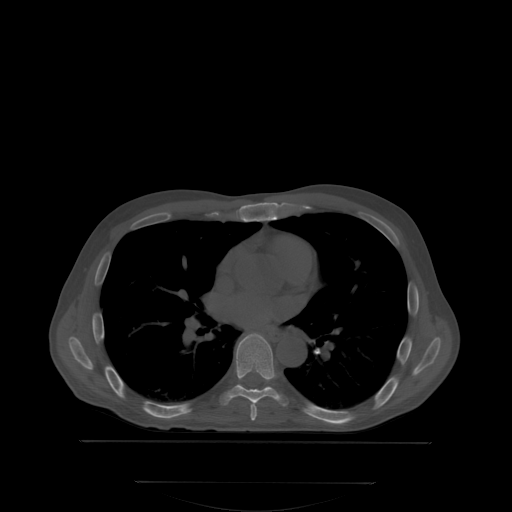
CT including the spine, one axial slice; position 226 of 350 along the scan axis; bone window (W 1800 / L 400 HU); 2.5 mm slice thickness; 512 × 512 image matrix, field of view 500 × 500 mm. Patient: male, 58 years. Case-level facts recorded for this patient, not image findings: primary cancer: prostate.
Structures marked on this image (semi-automatically segmented with operator editing):
- T6 vertebra: bounding box [x1, y1, x2, y2] px = [250, 405, 257, 420]
- T7 vertebra: [219, 333, 289, 406]